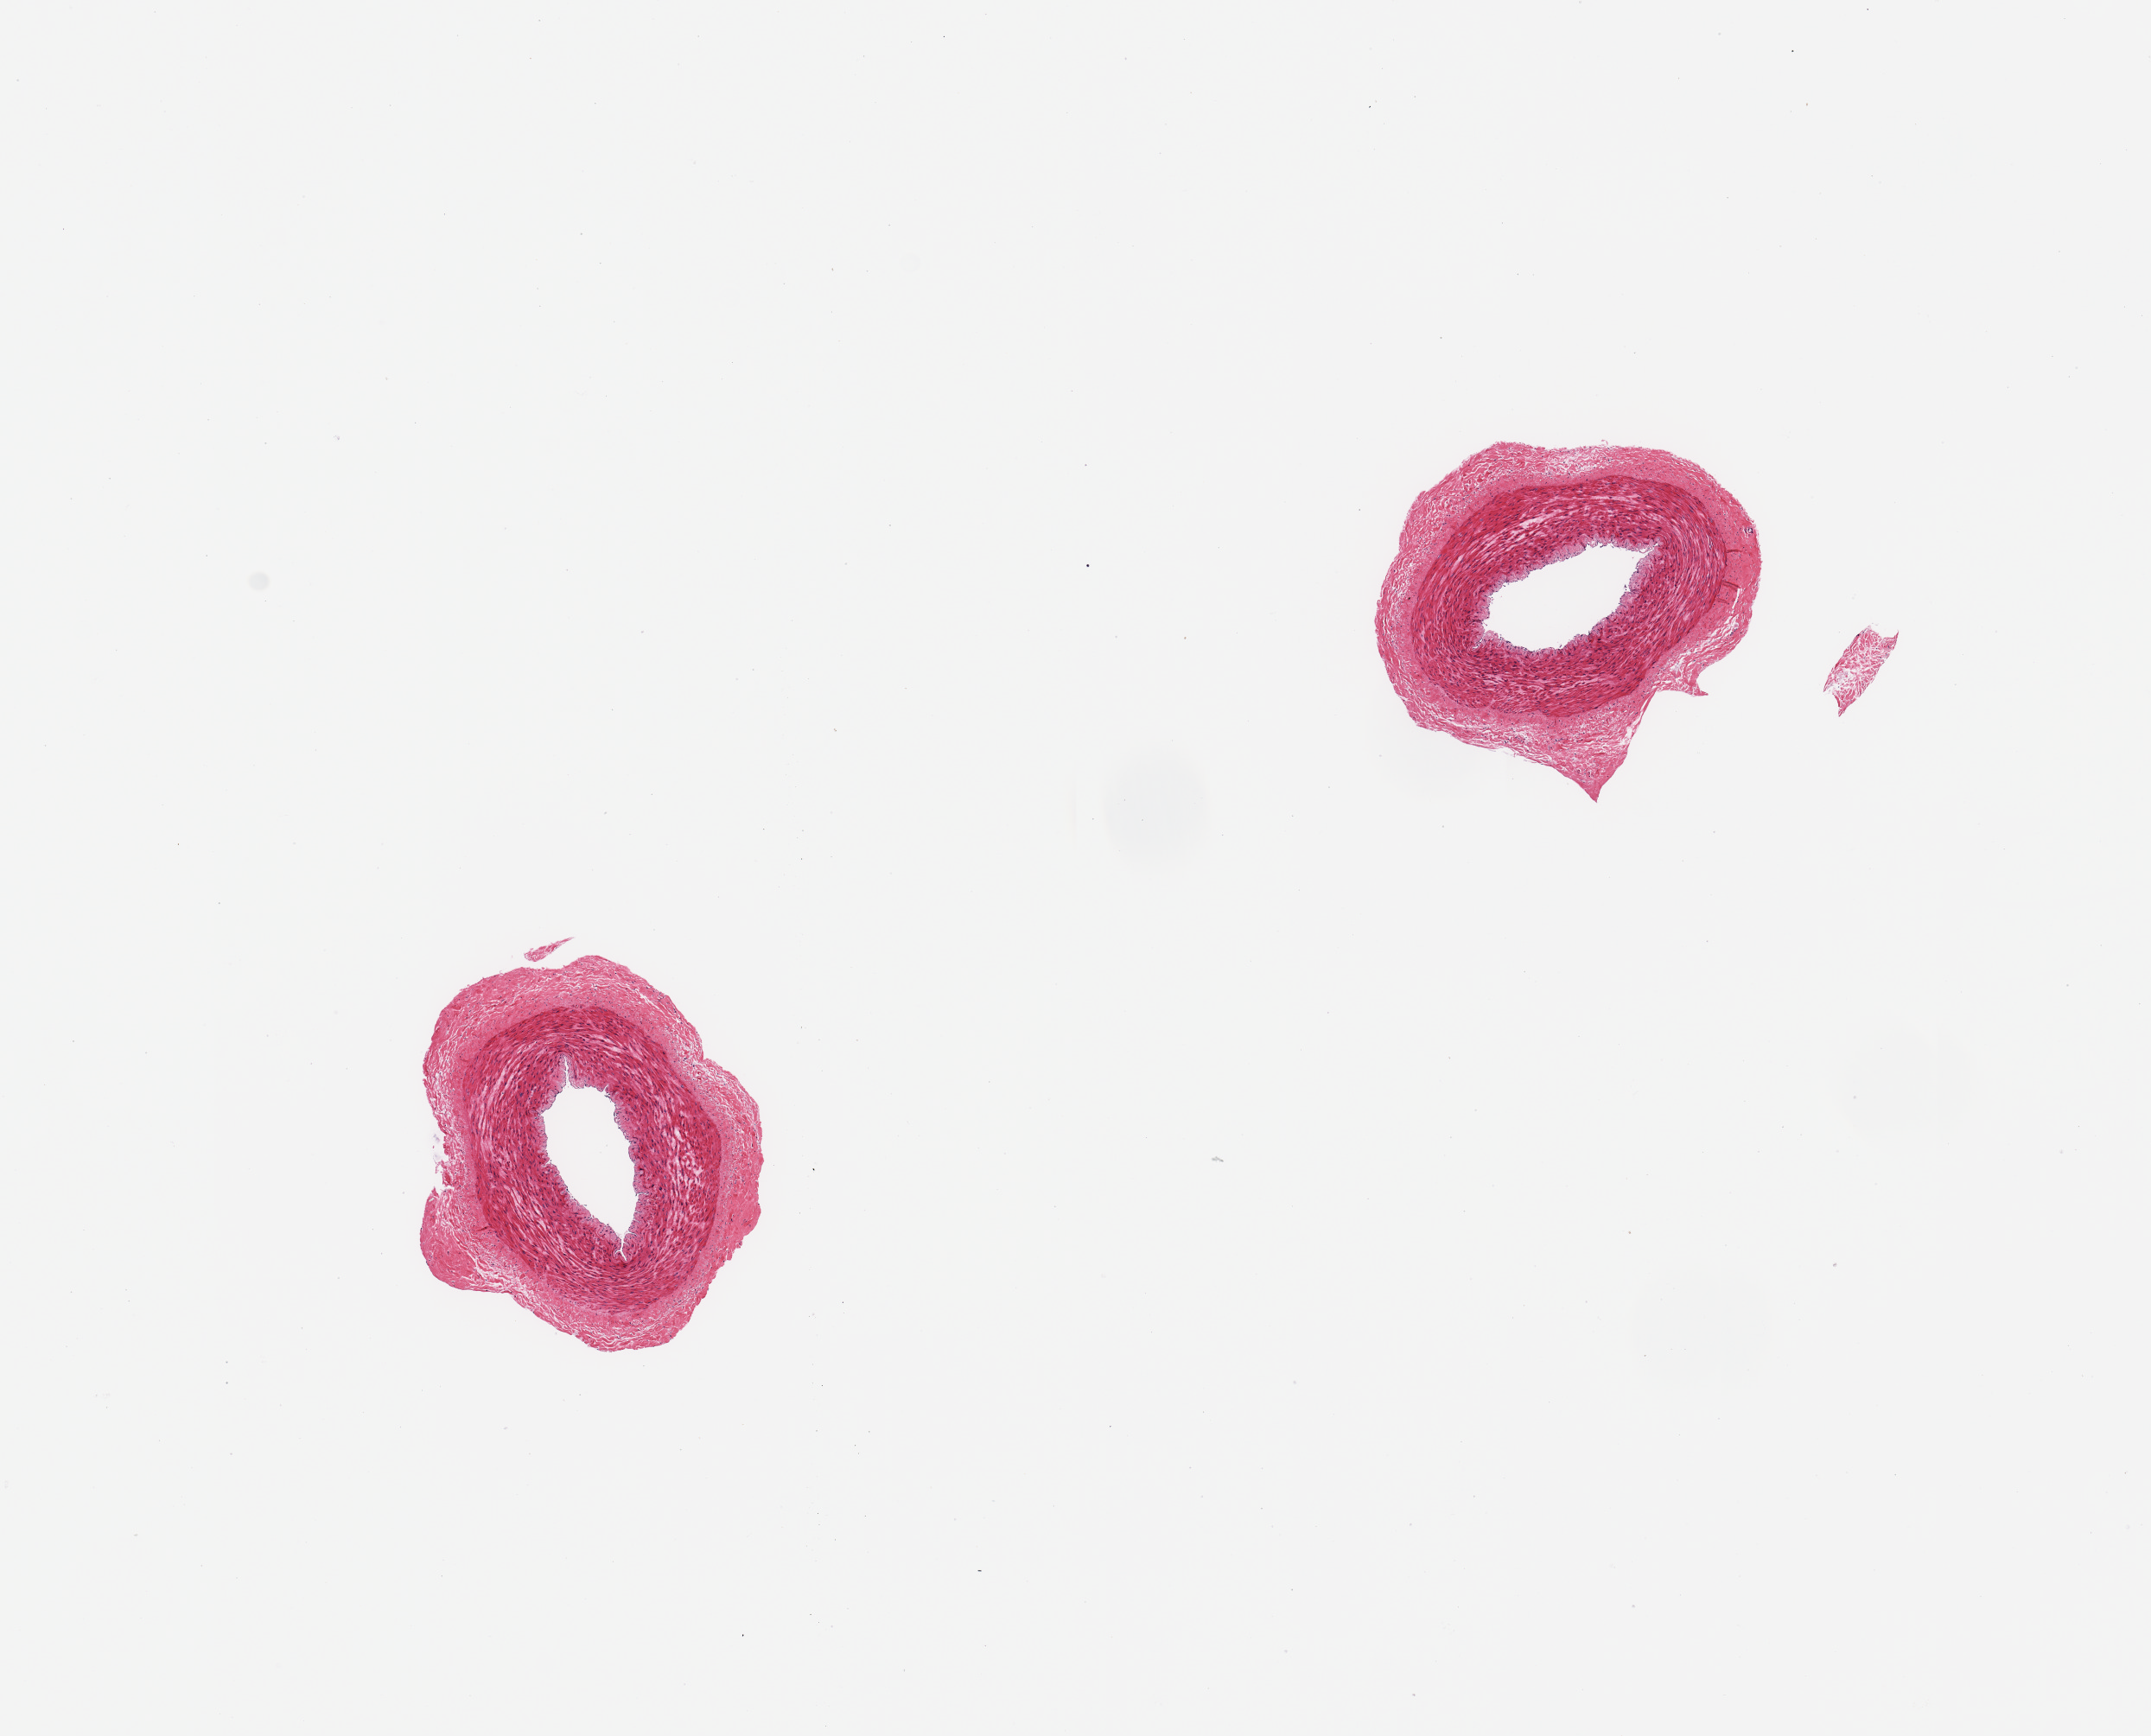
Digitized haematoxylin and eosin-stained section, brightfield — shown as a low-resolution overview of the whole scanned area (about 9.8 x 7.9 mm, acquisition: 20x scan). PAXgene-fixed paraffin-embedded (PFPE) section. Section of tibial artery (target tissue). Donor tissue sample. Male donor.
• reviewer comment on this tissue sample: 2 pieces; well trimmed, no extraneous tissues; no lesions